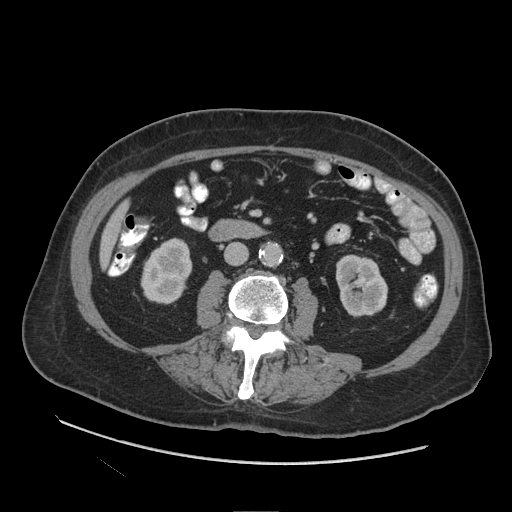
Contrast-enhanced abdominal CT (liver protocol), one axial slice; position 22 of 109 along the scan axis; soft-tissue window (W 400 / L 40 HU); 2.5 mm slice thickness; 512 × 512 image matrix, field of view 420 × 420 mm. From the clinical record (not read from this slice): diagnosis: hepatocellular carcinoma (patient treated with transarterial chemoembolisation; whether this scan precedes or follows treatment is not stated here); TNM stage (as recorded): Stage-I; Child-Pugh class: A; tumour nodularity: uninodular.
Annotated regions visible in this slice (semi-automatic segmentation, software-assisted and operator-edited):
- liver parenchyma outside the tumour (the mass and vessels are separate outlines, so this box may not span the whole liver): bounding box (x1, y1, x2, y2) in pixels: (100, 202, 127, 266)